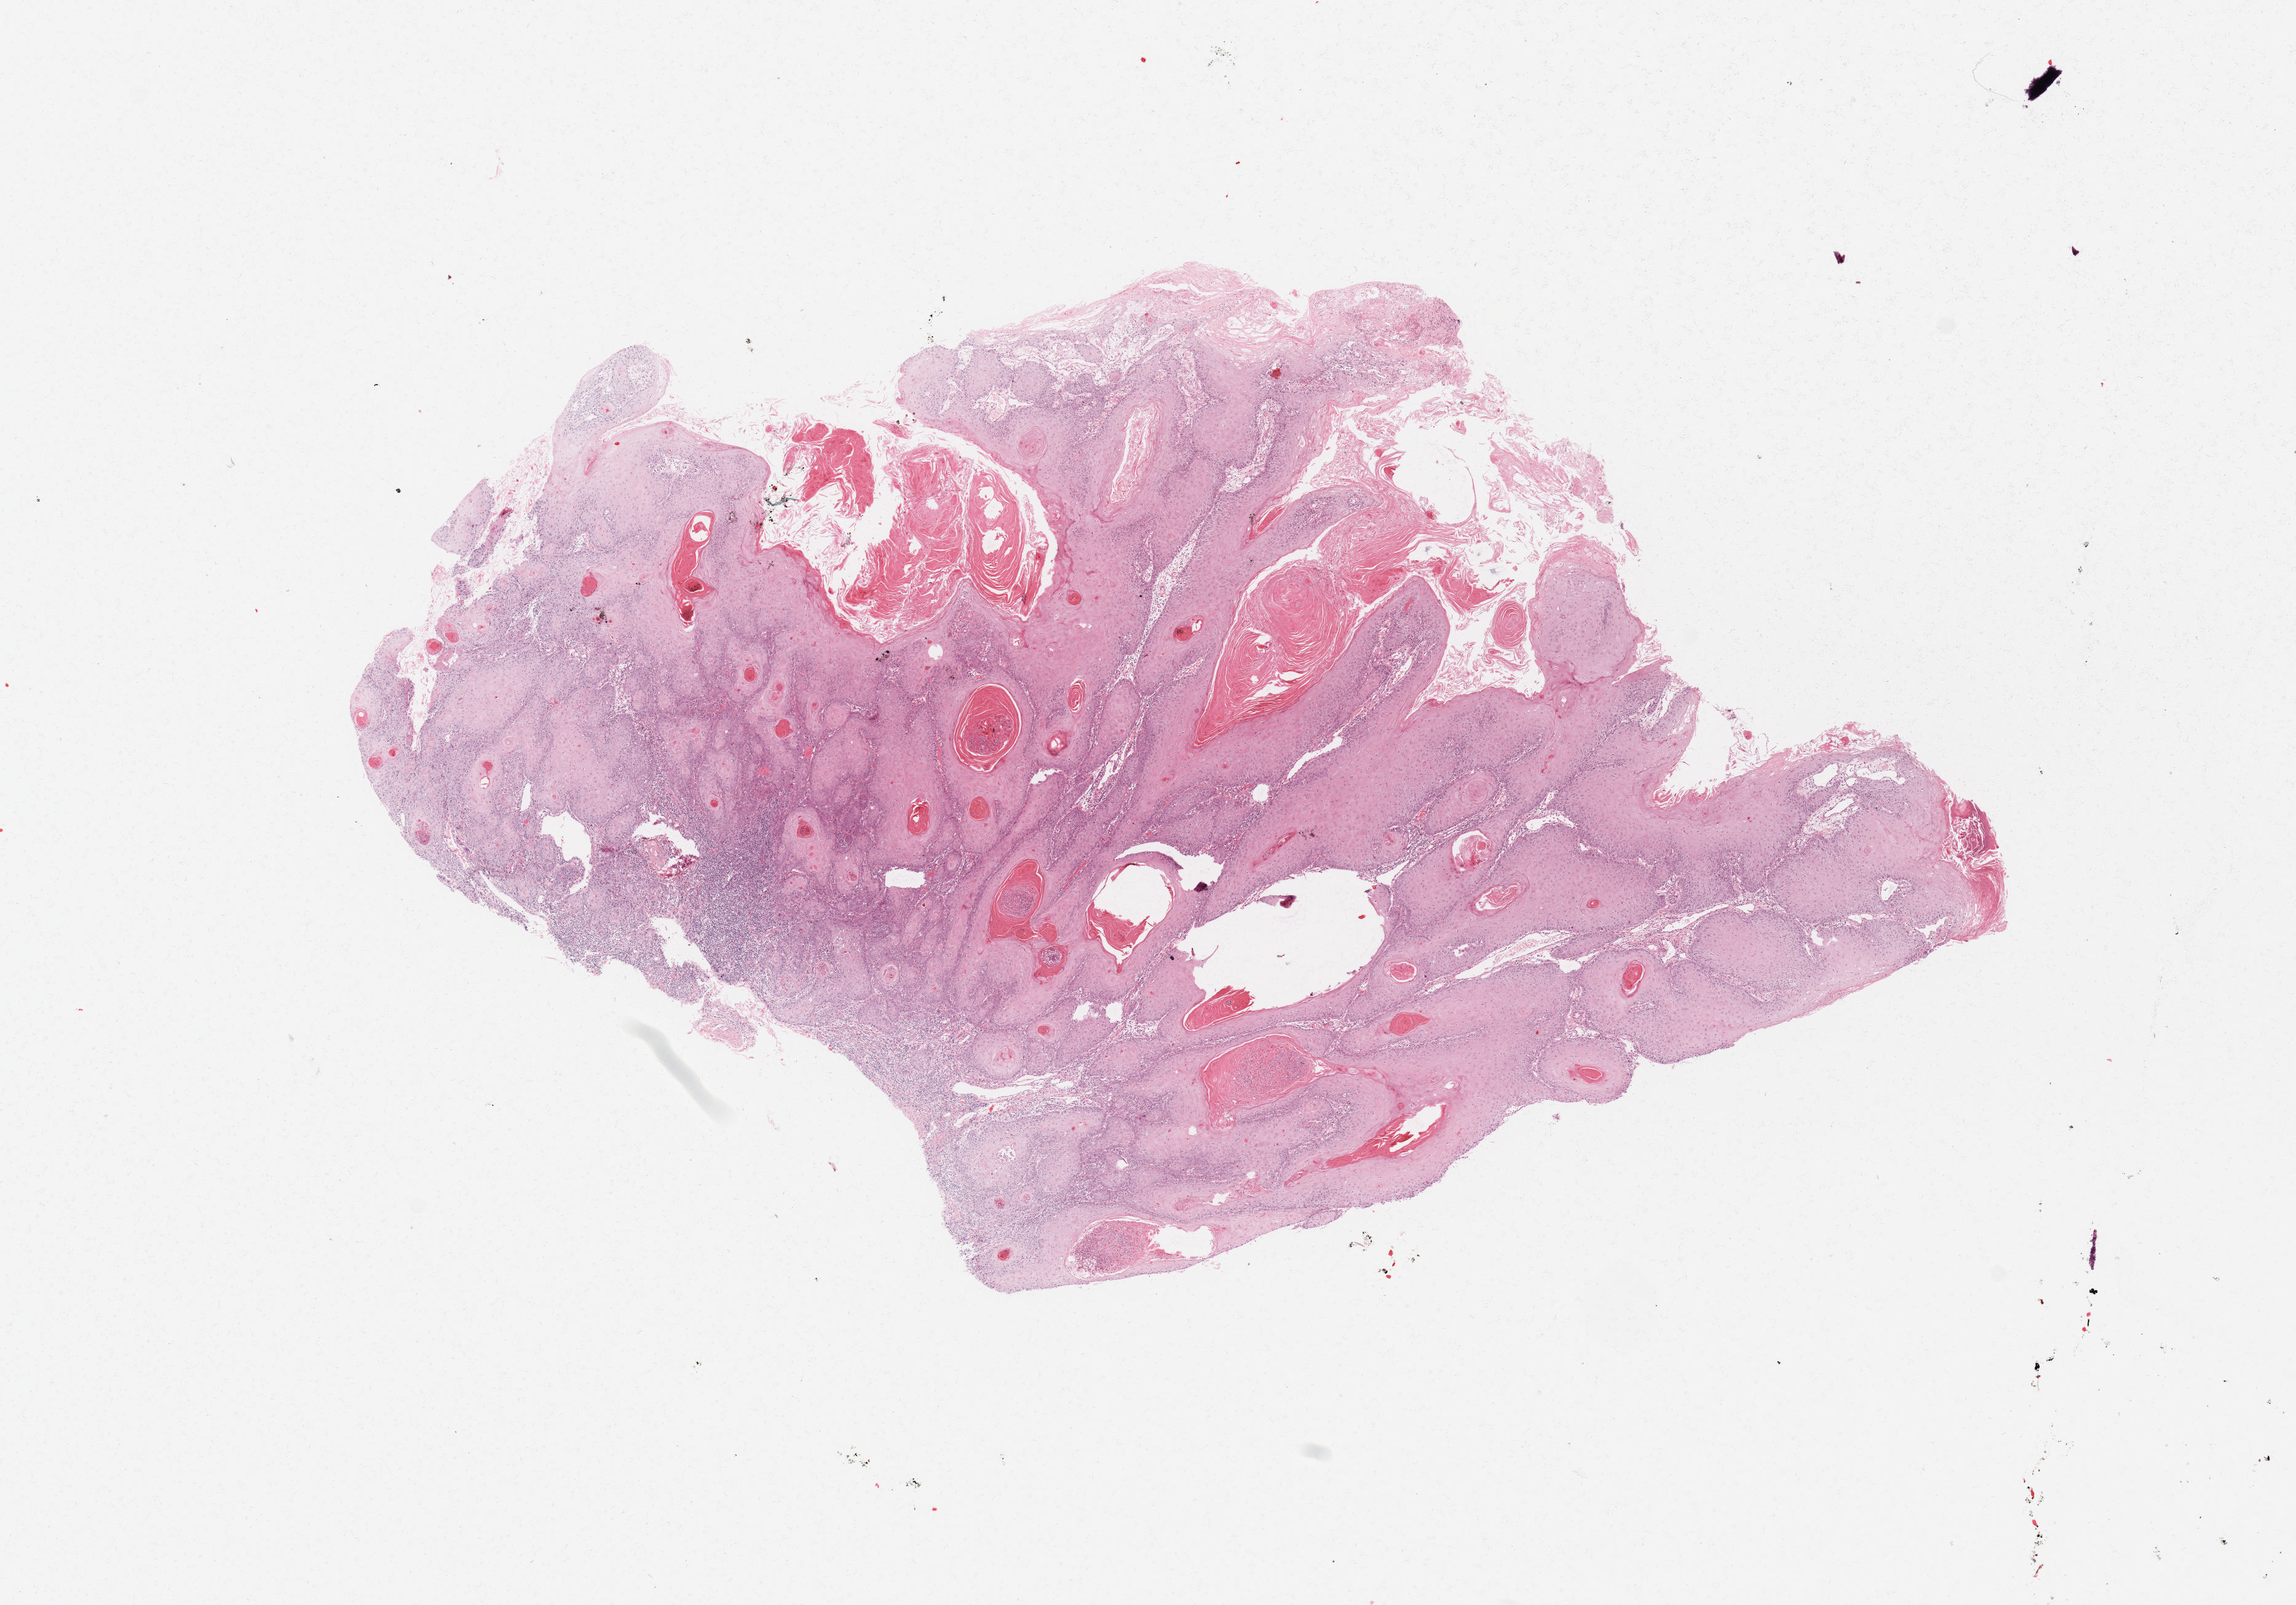
Hematoxylin and eosin (H&E) stained whole-slide image — a low-resolution overview of the entire scanned area, about 14.8 x 10.3 mm (from a 20x scan). Tumour tissue sample, sampled site: lip. 54-year-old male patient. Histologic grade: G1 (well differentiated). Composition of this section per pathologist review: tumour nuclei 85%, necrosis 3%.
• primary tumour site (as recorded): lip
• histologic diagnosis: Squamous cell carcinoma, NOS (lip, NOS)
• AJCC pathologic stage: III